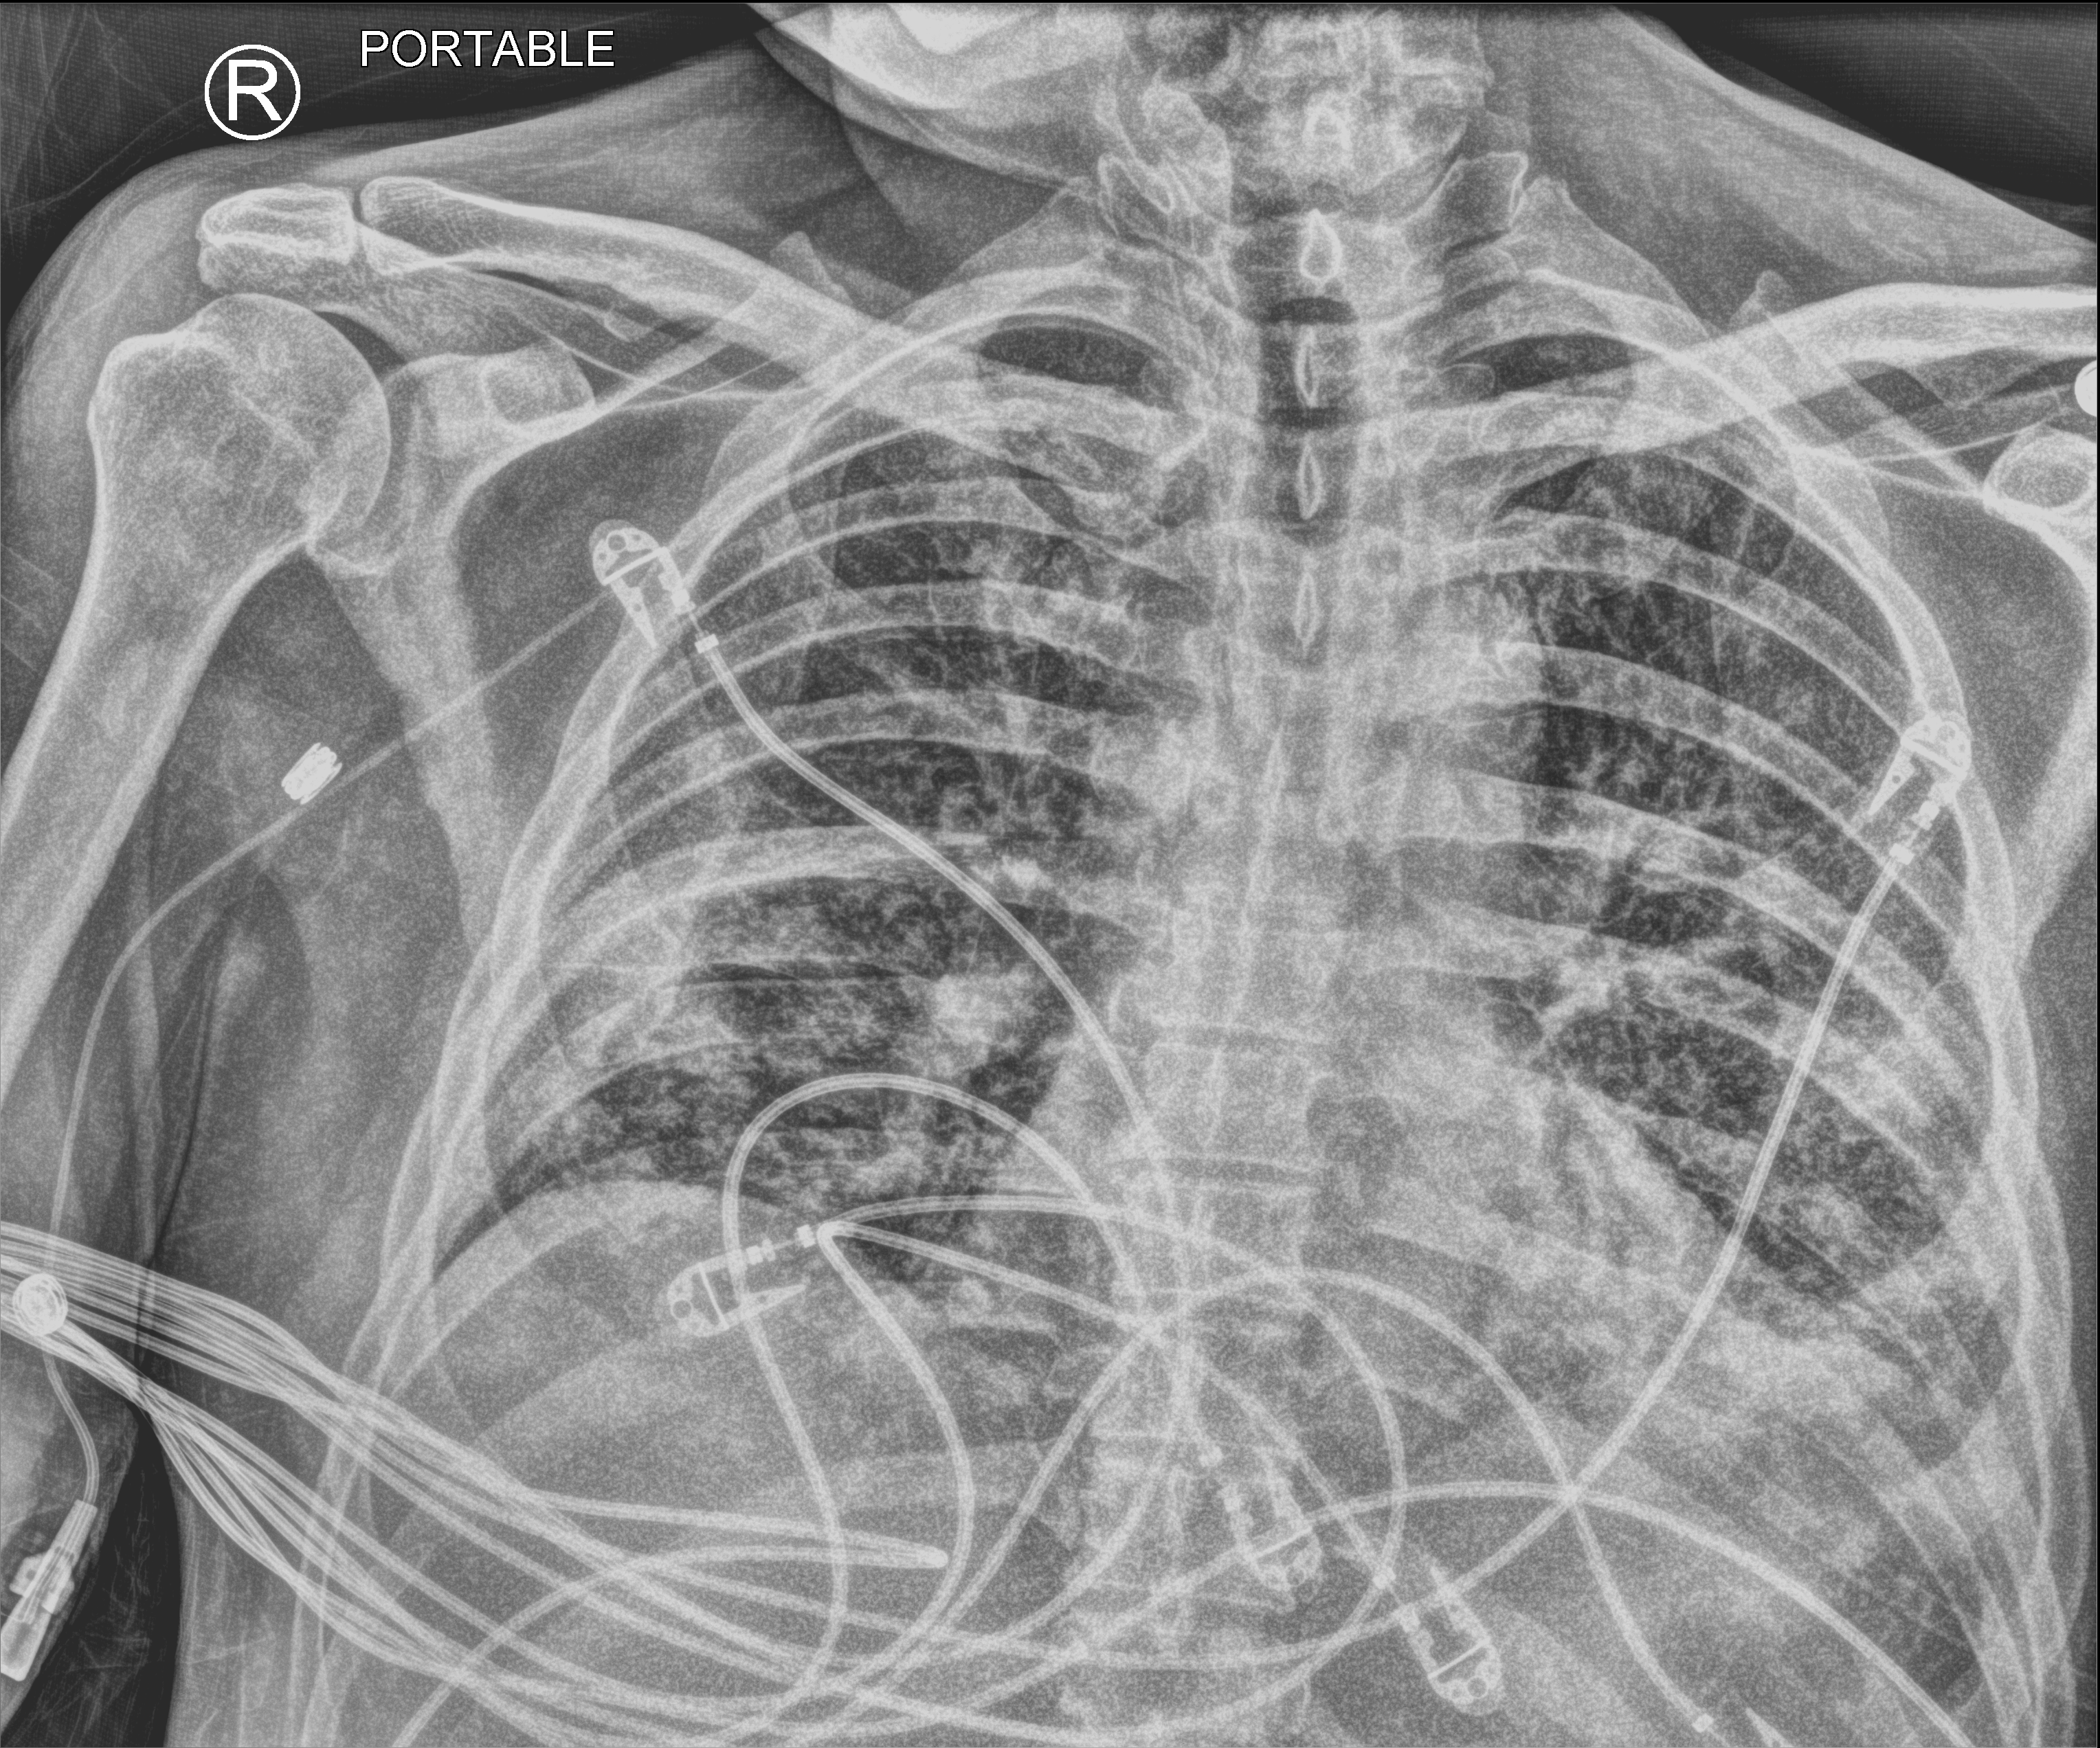
Portable chest radiograph, anteroposterior (AP) projection. Patient hospitalised with COVID-19; male, aged 60–74 years.
Hospital-stay facts (about this admission, not read from this image; timing relative to this image not recorded):
- mechanically ventilated during this hospital stay: yes